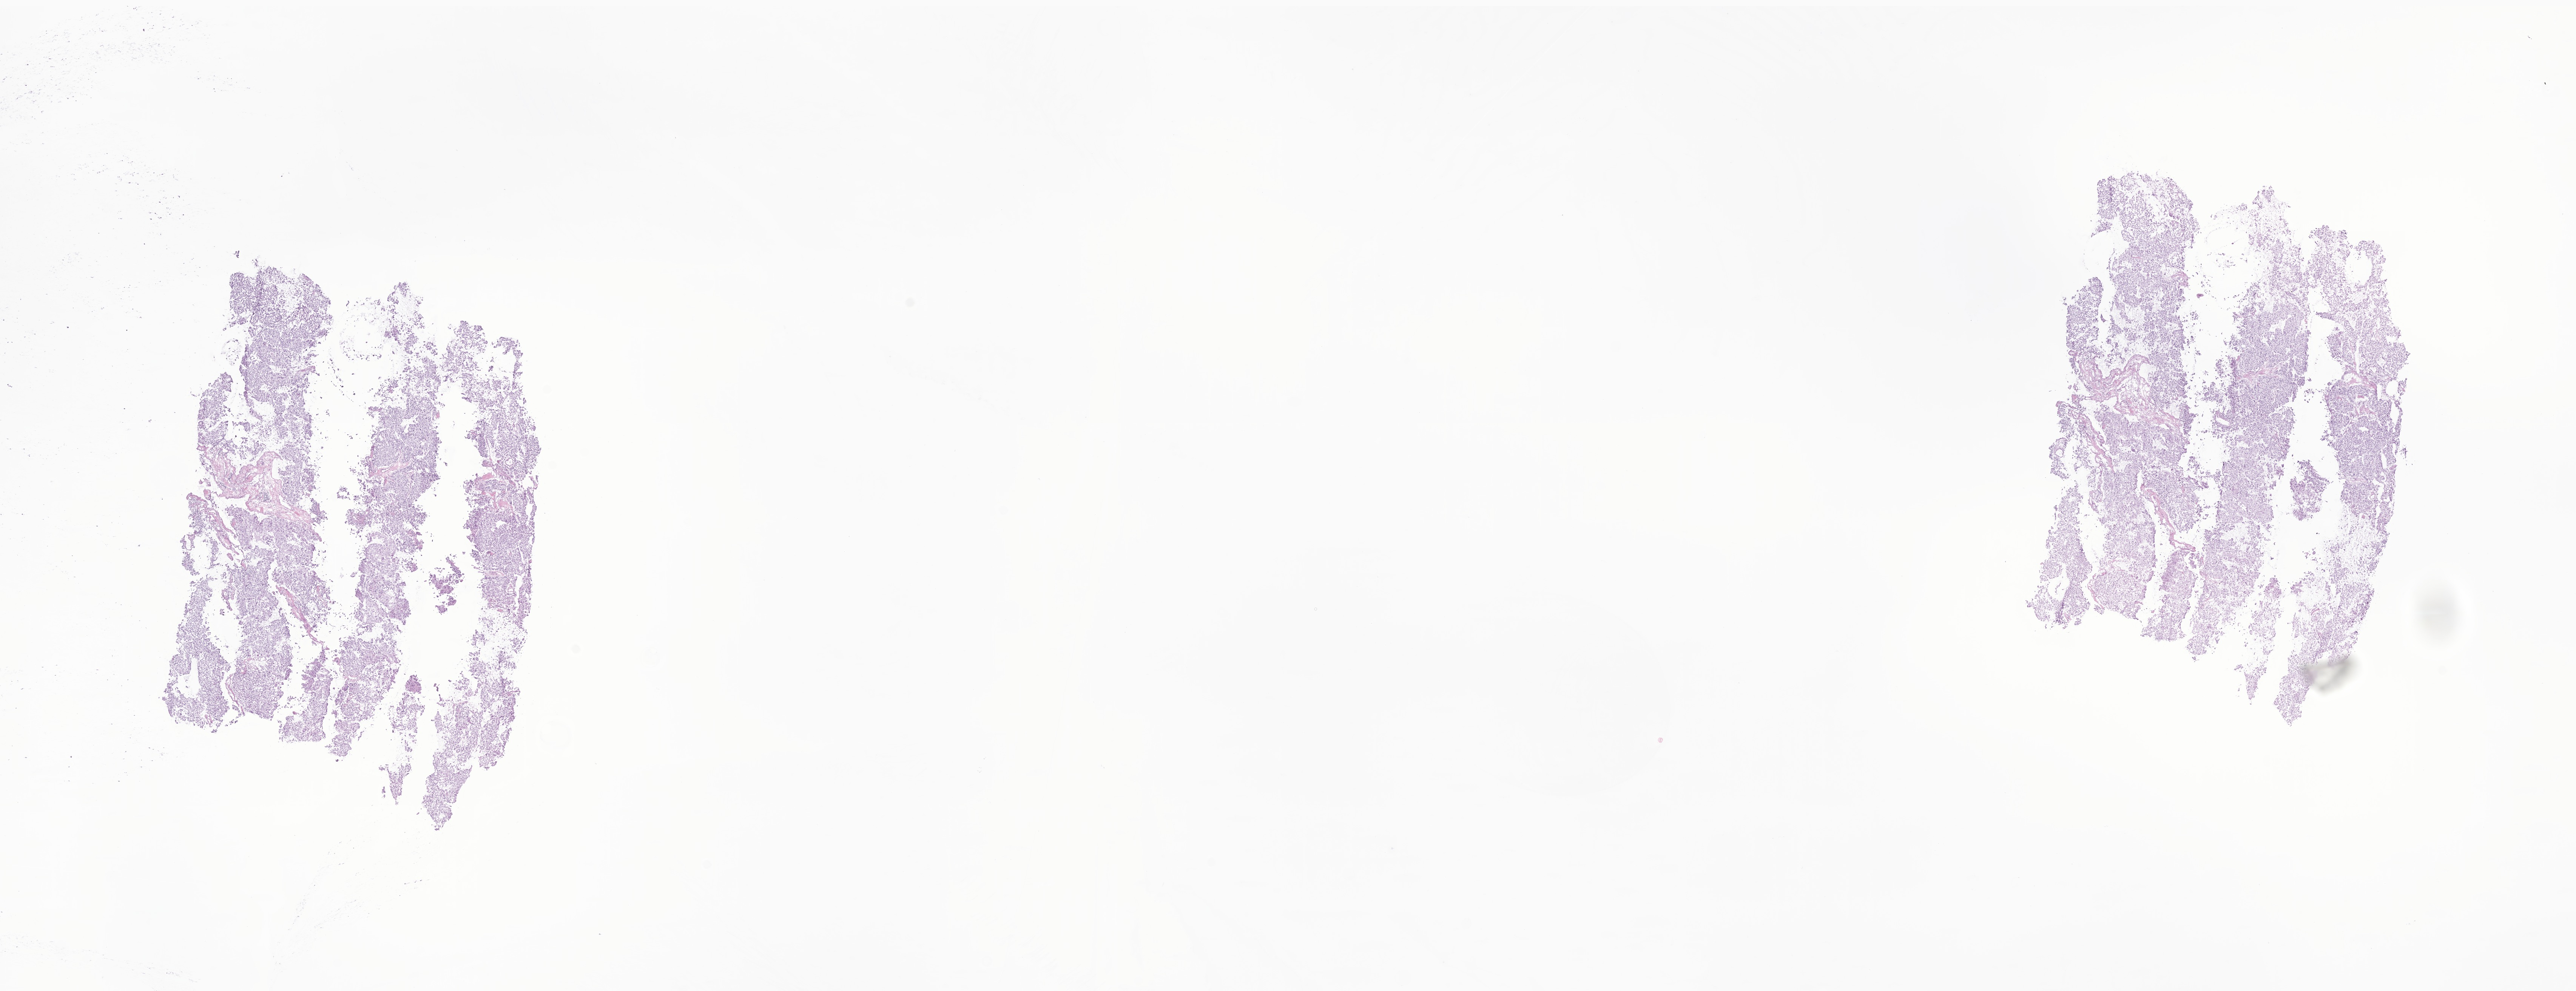
Digitized haematoxylin and eosin-stained section of tumor tissue from the adrenal gland — whole scanned area (about 28.8 x 11.1 mm) shown as a low-resolution overview. Patient: male, age 248 months.
Specimen: frozen section.